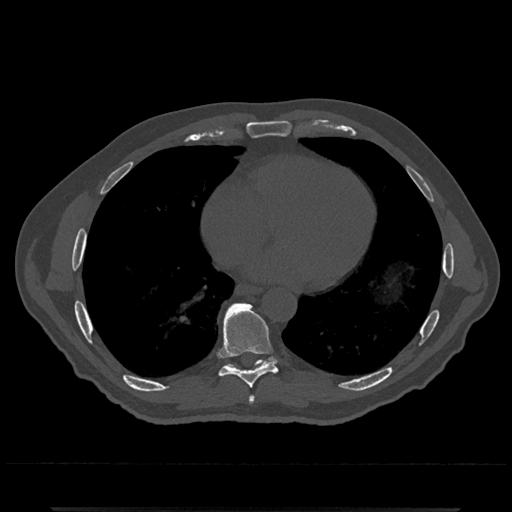
CT including the spine, one axial slice. Slice 660 of 797 in the series (ordered by position). Reconstruction kernel Br40s/3. 120 kVp. Bone window (W 1800 / L 400 HU). 512 × 512 image matrix, field of view 393 × 393 mm. Patient: male, 67 years. Case-level facts recorded for this patient, not image findings: primary cancer: prostate.
Structures marked on this image (semi-automatic segmentation, software-assisted and operator-edited):
- T7 vertebra: box from (x=248, y=395) to (x=254, y=404) px
- T8 vertebra: (x=217, y=302)–(x=278, y=389)
- T9 vertebra: (x=225, y=302)–(x=277, y=369)